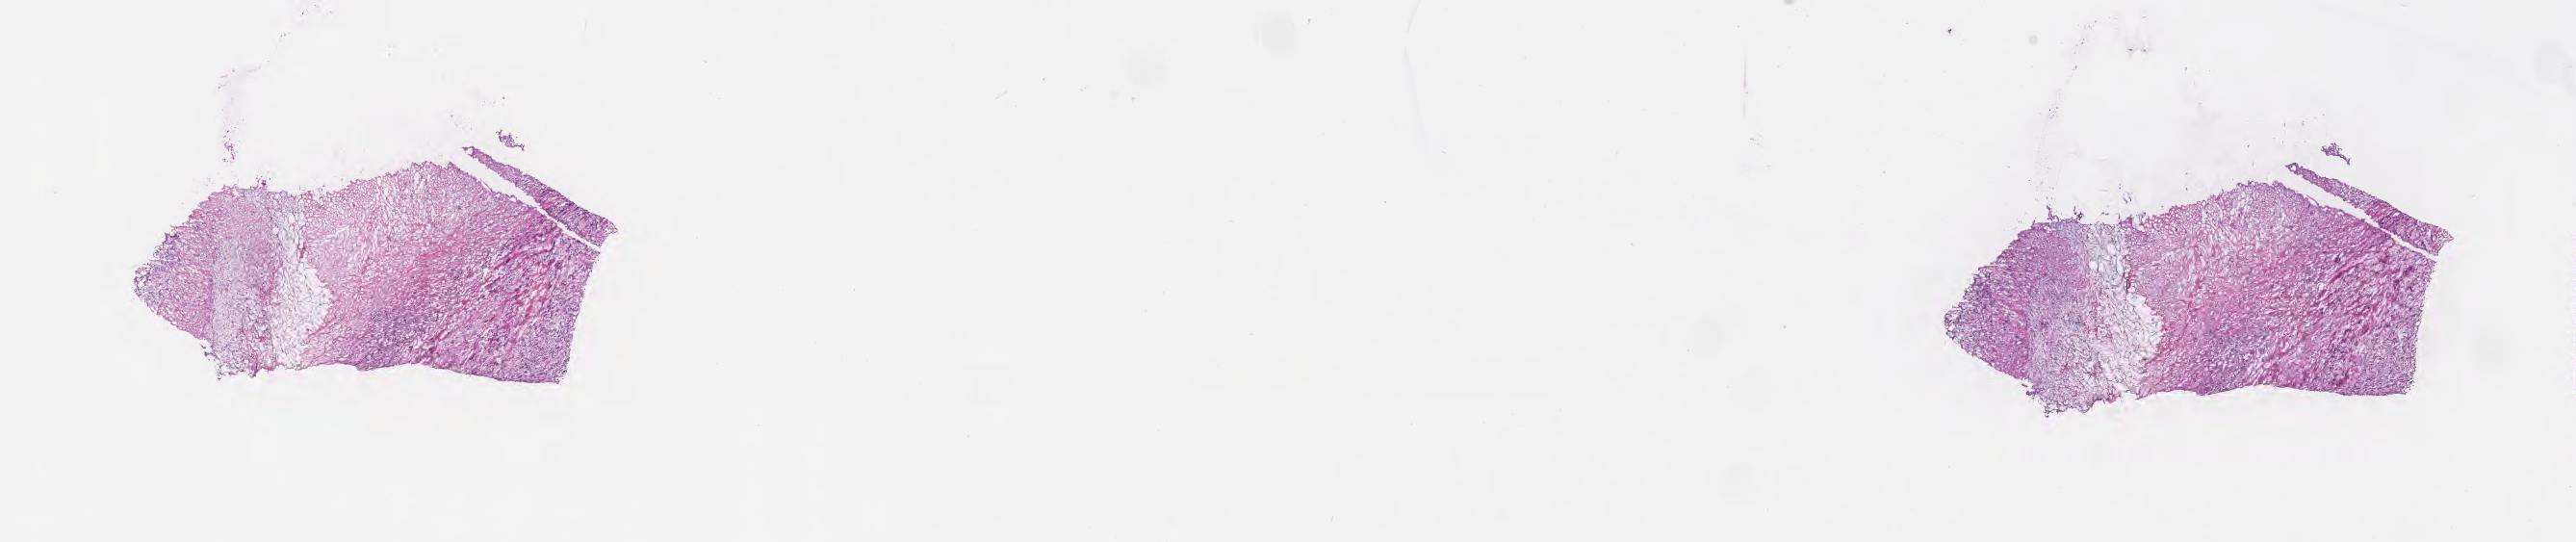
Digitized hematoxylin and eosin (H&E)-stained section, low-resolution overview of the scanned area, about 21.6 x 4.6 mm, frozen section, specimen: metastatic tumor tissue, resected from lymph node. Female patient; age at initial diagnosis 78 years. Slide review estimates, as recorded: tumor cells 70%, tumor nuclei 70%, stromal cells 30%, necrosis 0%, normal cells 0%. Infiltration values recorded for this section: lymphocyte infiltration 5%, monocyte infiltration 3%, neutrophil infiltration 6%.
- section: top of the tissue portion
- patient diagnosis (primary): Malignant melanoma, NOS